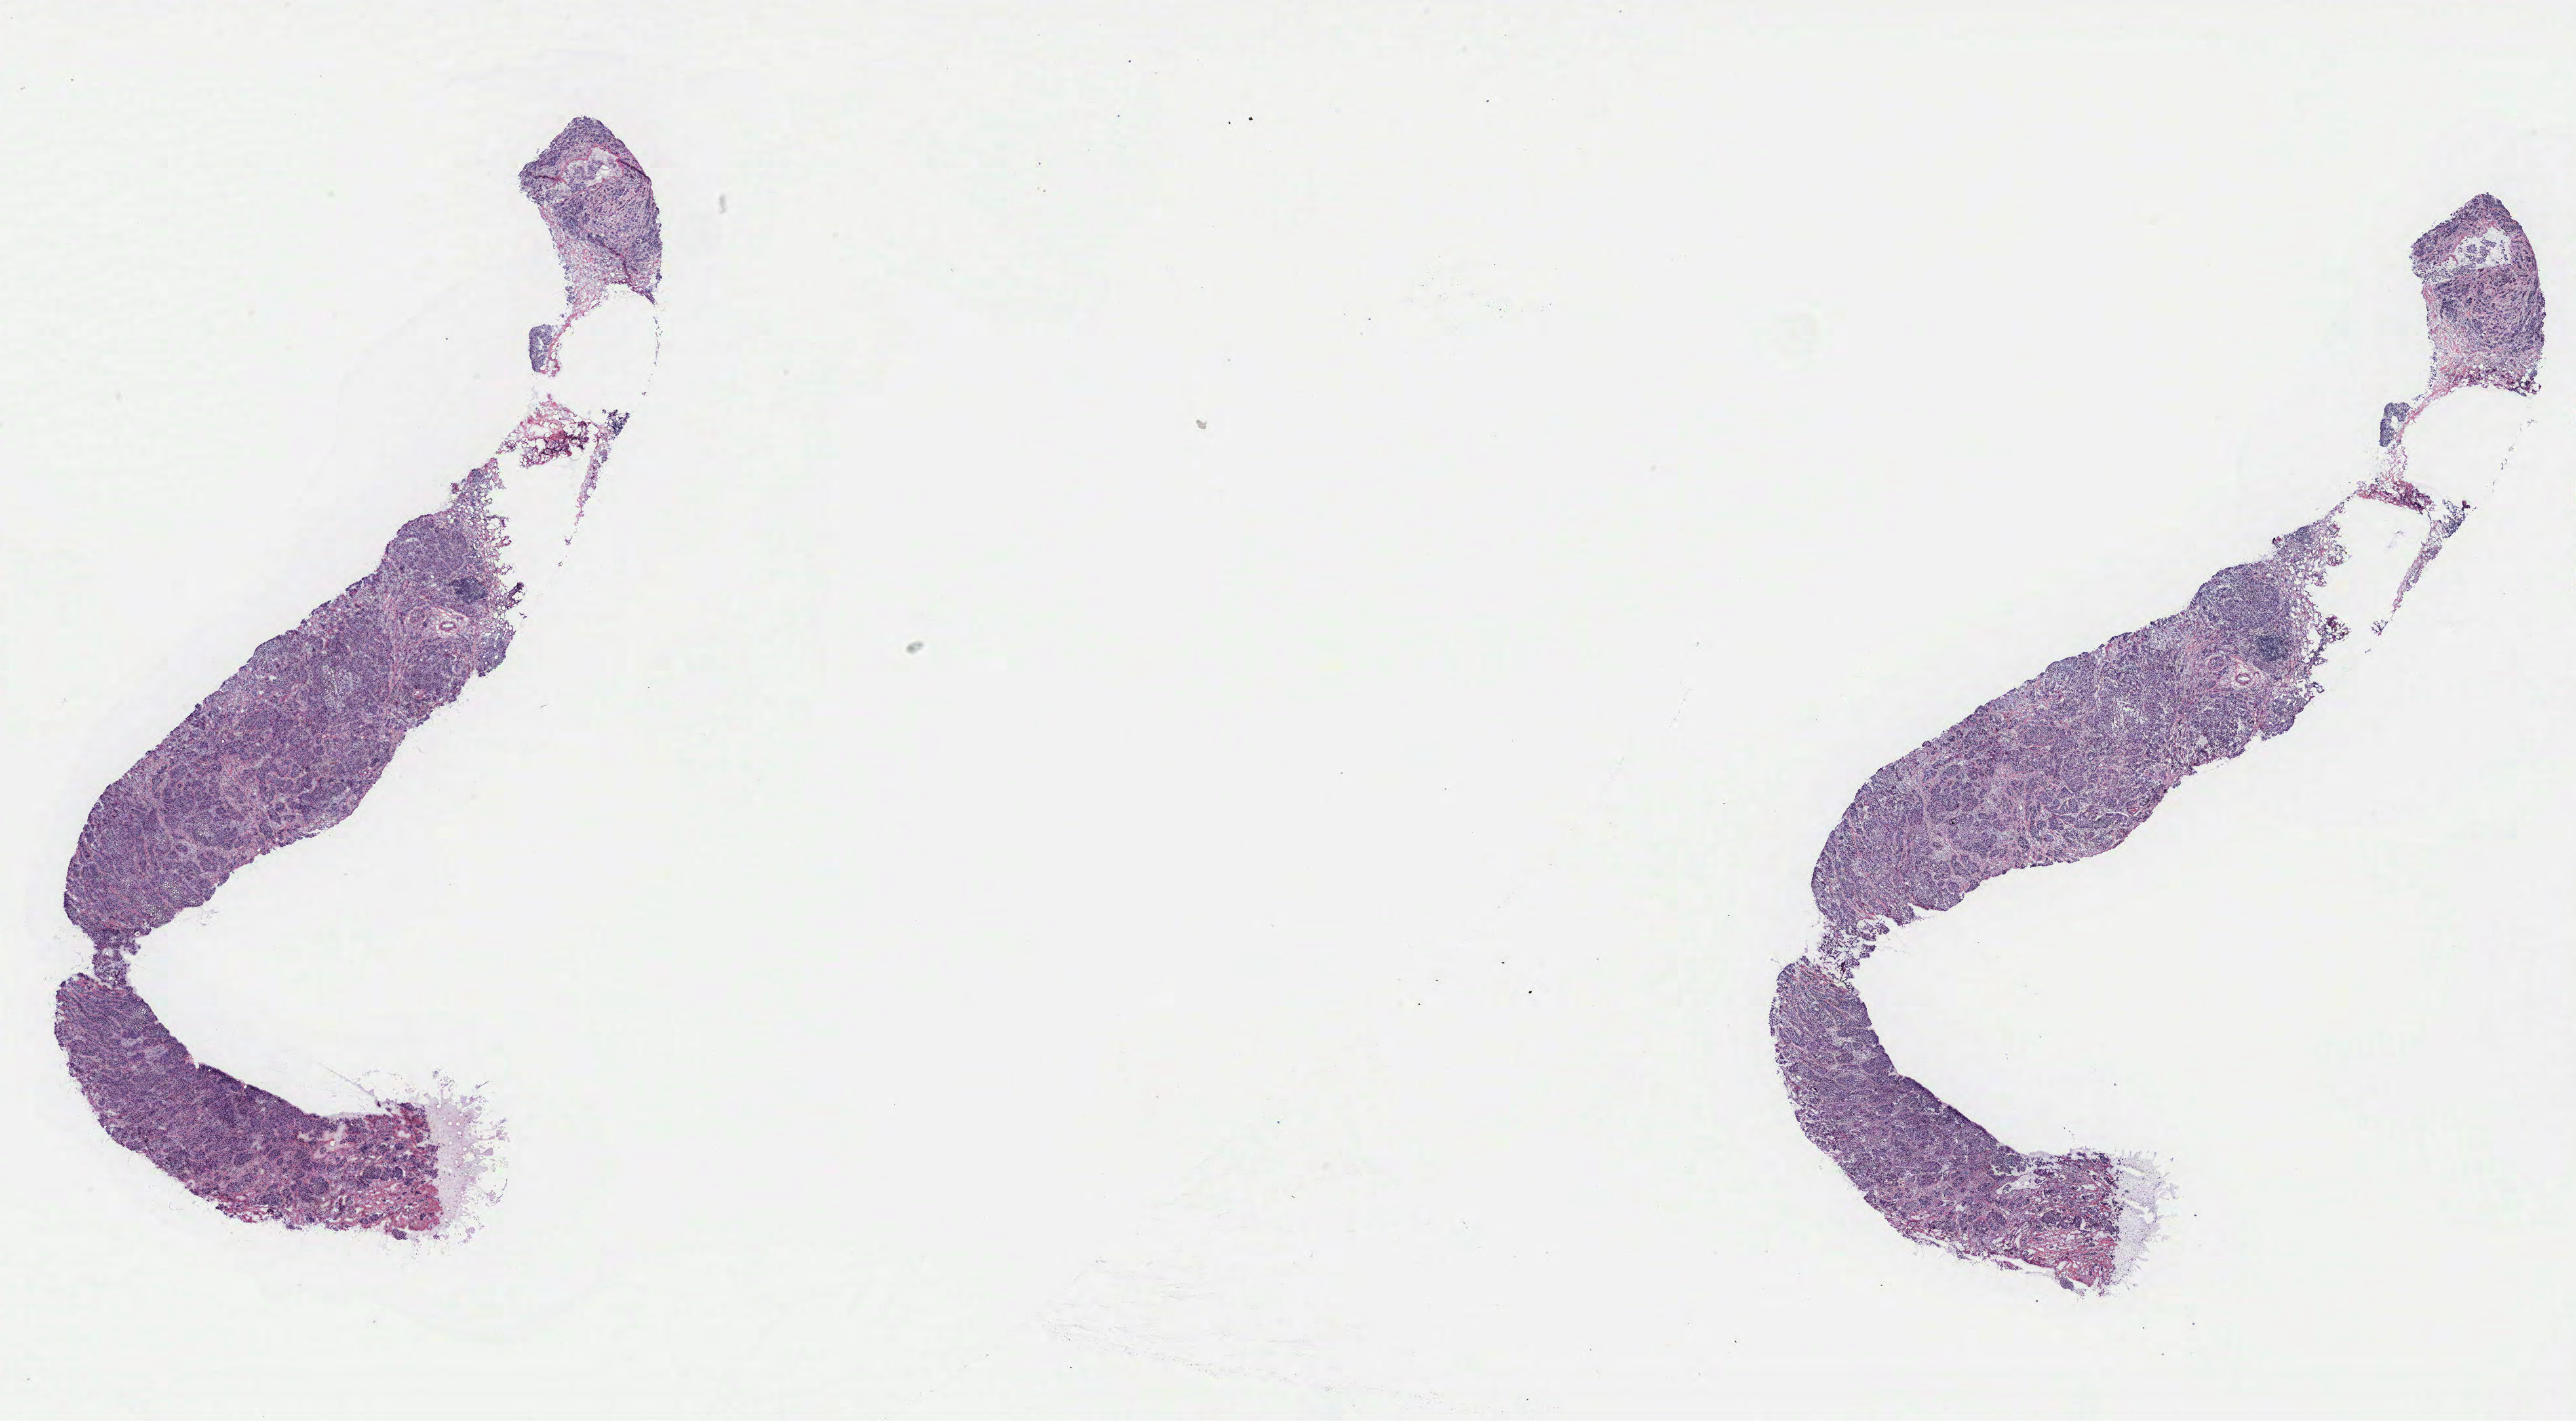
H&E whole-slide image — a low-resolution overview of the entire scanned area, about 31.5 x 17.4 mm (slide scanned at 40x); tumour tissue sample, breast. 55-year-old female patient.
* histologic diagnosis: Infiltrating duct carcinoma, NOS
* AJCC pathologic stage: IIB